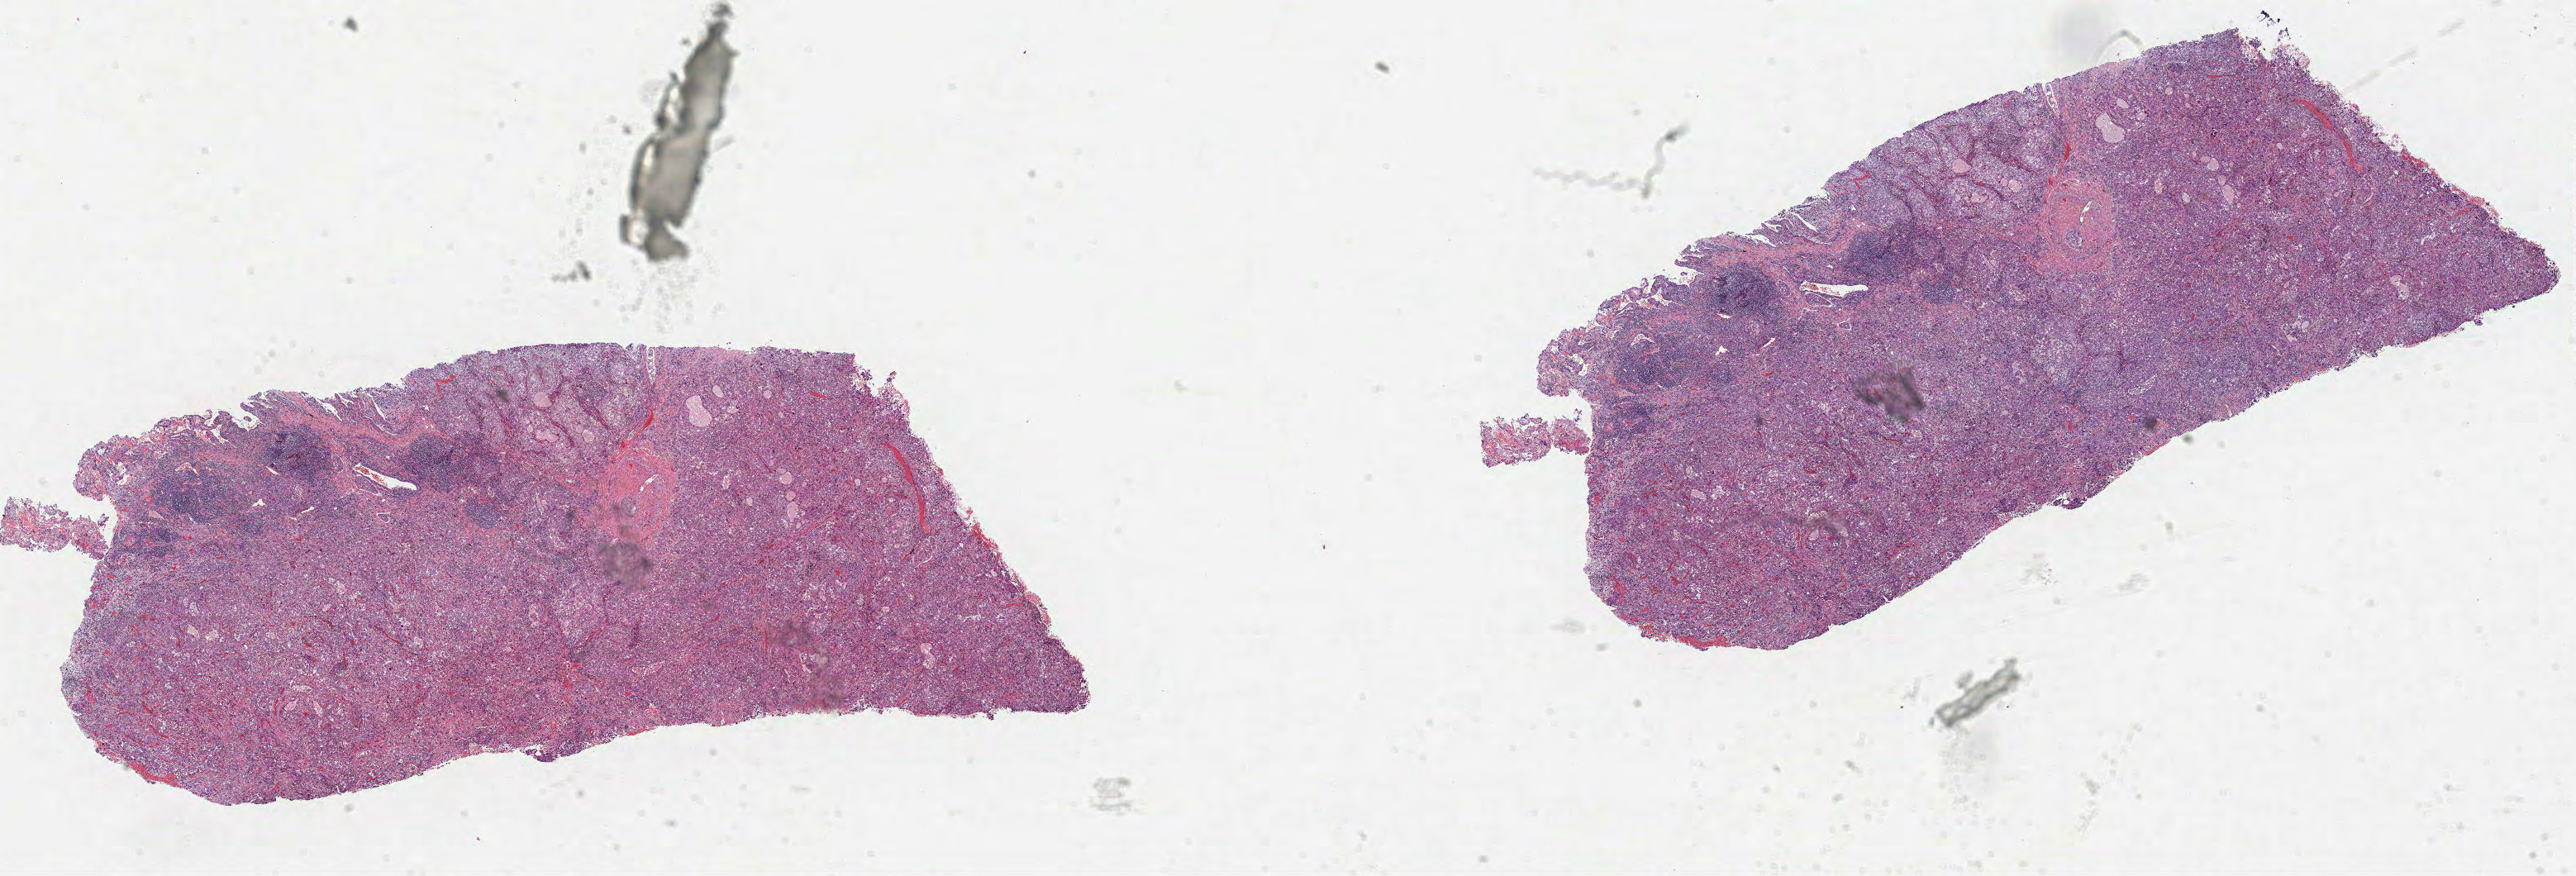
H&E-stained whole-slide image, a low-resolution overview of the entire scanned area, about 25.1 x 8.5 mm. FFPE section. Lung, primary tumour sample. Patient: female, age at initial diagnosis 62 years.
Histologic diagnosis: Adenocarcinoma, NOS (upper lobe, lung). AJCC pathologic stage: IA (7th edition). Laterality: right.